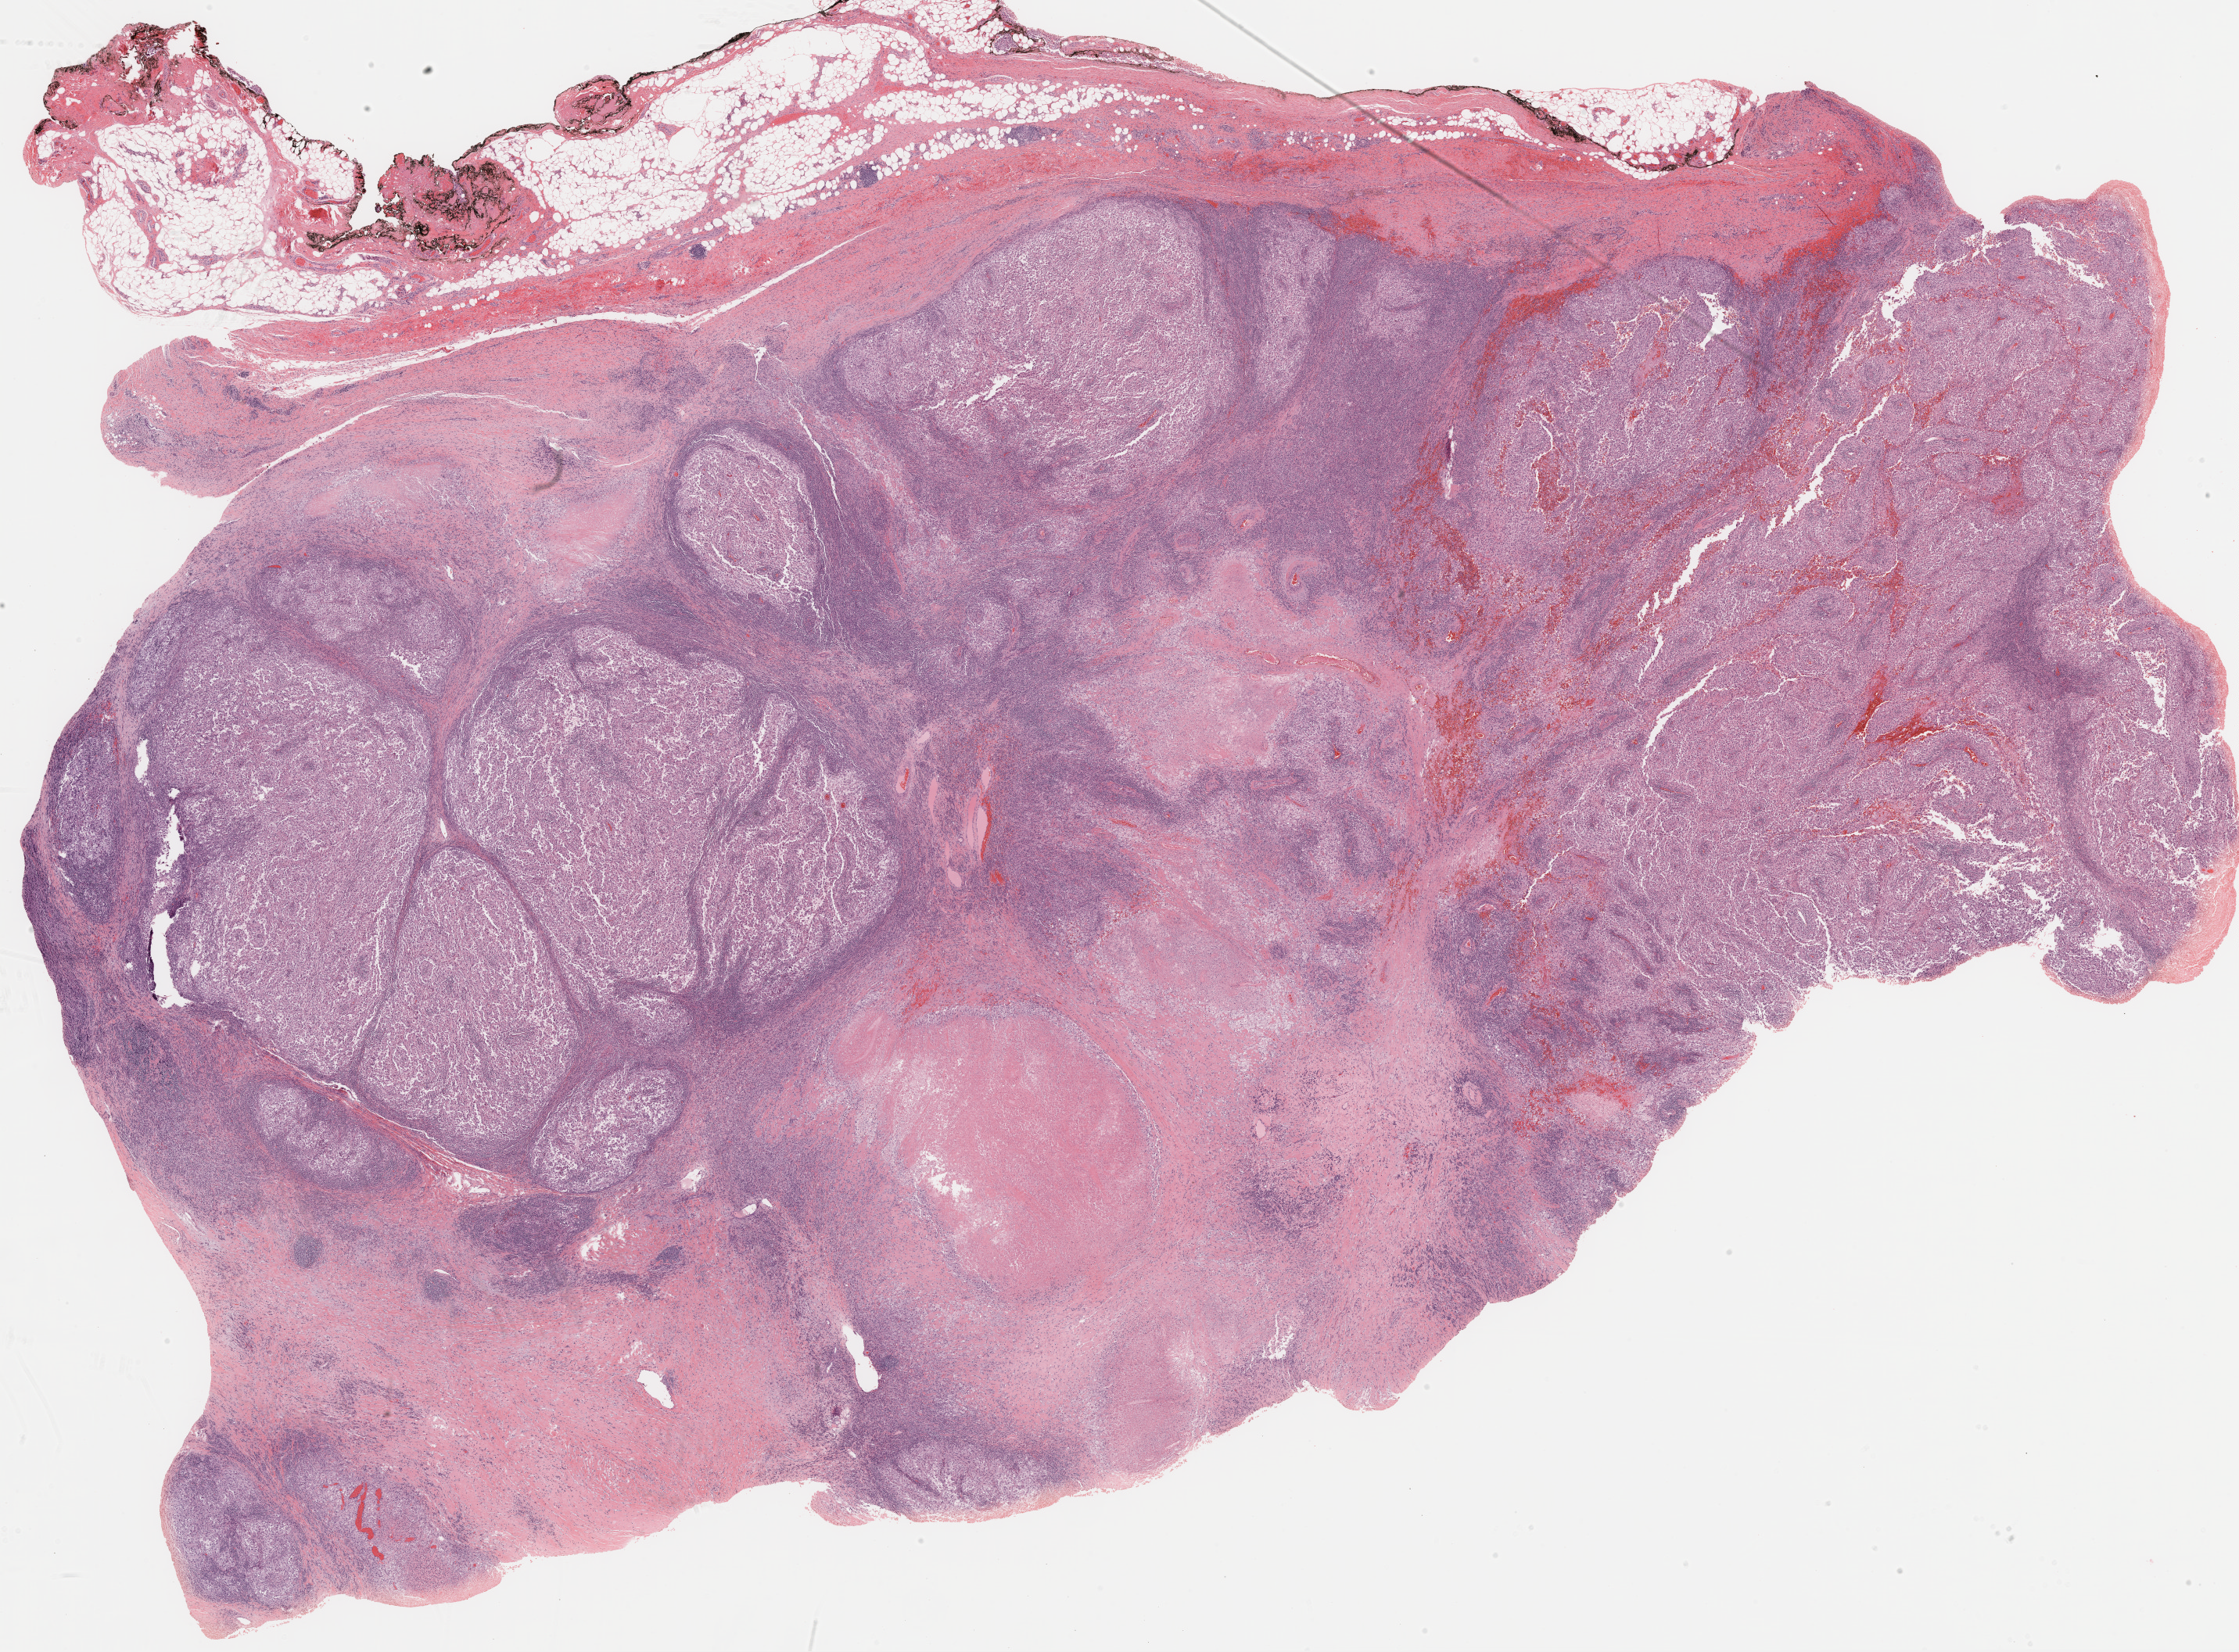
H&E whole-slide image, a low-resolution overview of the entire scanned area, about 23.1 x 17.0 mm (slide scanned at 20x); formalin-fixed paraffin-embedded (FFPE) diagnostic section; metastatic tumour sample, sampled site: connective, subcutaneous and other soft tissues. Male, age 42 years at initial diagnosis.
* this section: metastatic tumour tissue
* patient diagnosis: Malignant melanoma, NOS